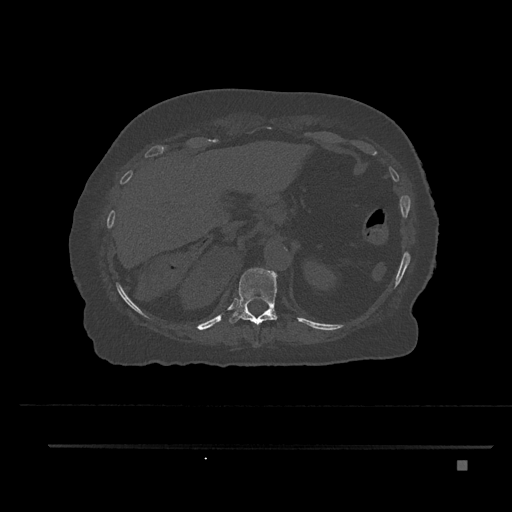
CT including the spine, one axial slice. Position 312 of 797 along the scan axis. Reconstruction kernel Br40s/3. 120 kVp. Bone window (W 1800 / L 400 HU). 512 × 512 image matrix, field of view 437 × 437 mm. Patient: female, 76 years. Case-level facts recorded for this patient, not image findings: primary cancer: lung.
Outlined on this slice (semi-automatic segmentation, software-assisted and operator-edited):
- T10 vertebra: bounding box (x1, y1, x2, y2) in pixels: (256, 341, 258, 346)
- T11 vertebra: (229, 268, 278, 326)